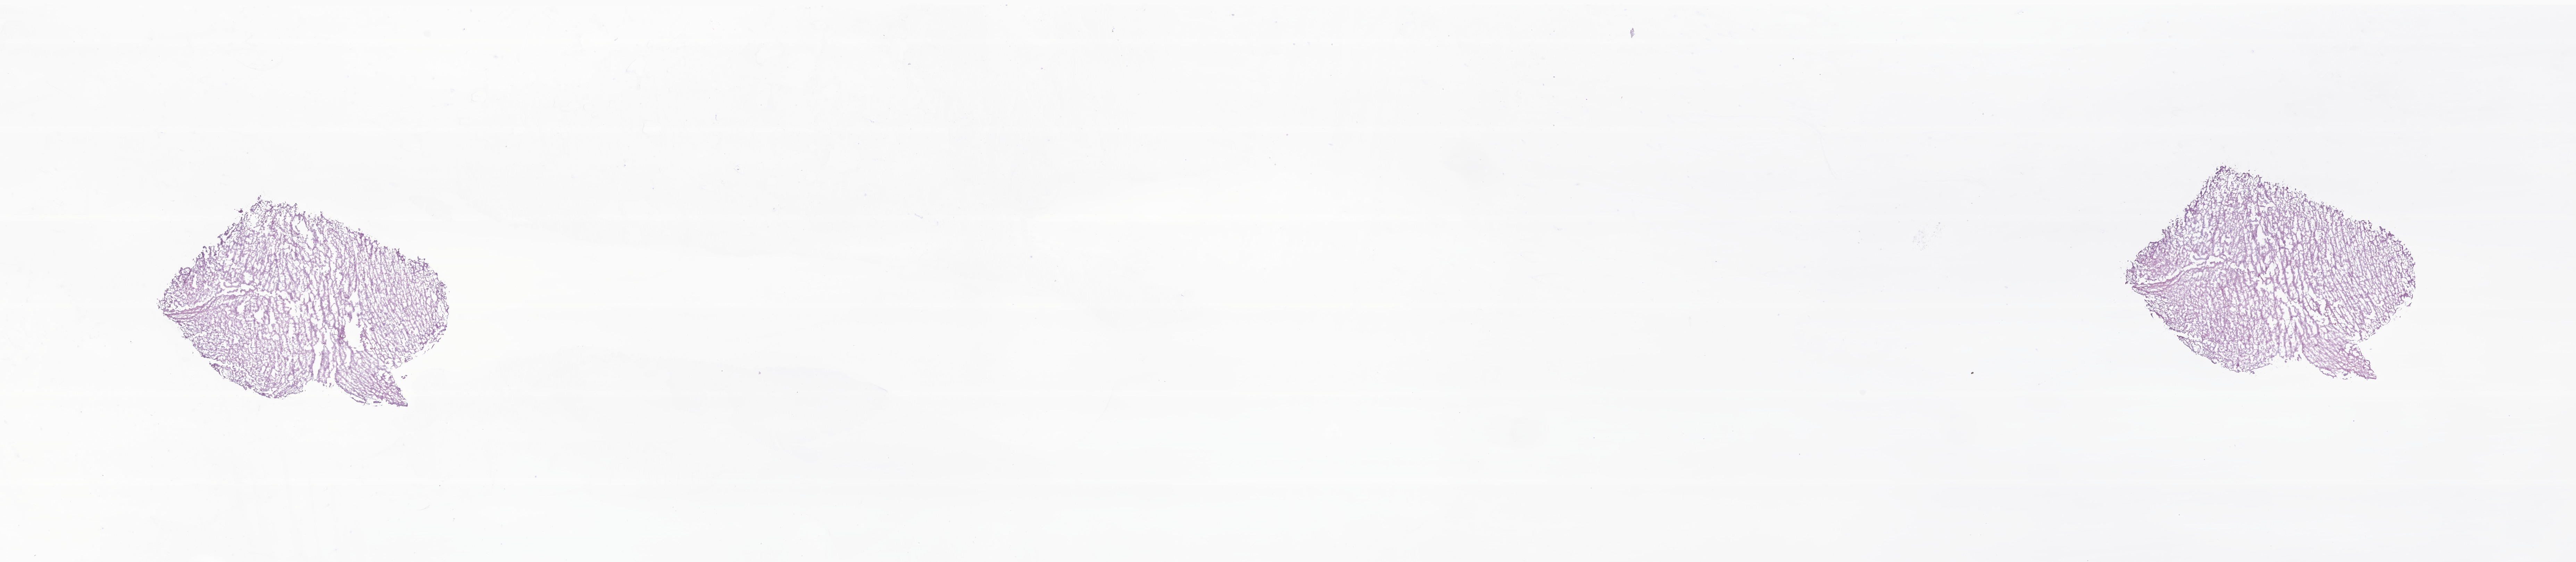
Whole-slide image, haematoxylin and eosin stain of tumor tissue from the spinal cord — low-resolution overview of the scanned area, about 31.3 x 6.8 mm, cryosection (OCT / tissue freezing medium). Female patient, age 196 months.
Diagnosis: Pilocytic astrocytoma.